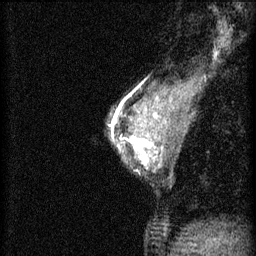
Breast MRI (dynamic contrast-enhanced), one sagittal slice; position 36 of 46 along the scan axis; 3 images stored at this slice position (order not interpretable as contrast timing); 1.5 T; TE 4.2 ms, TR 8.2 ms; 256 × 256 image matrix, field of view 180 × 180 mm. Patient: female, 44 years.
Annotated regions visible in this slice (semi-automatic segmentation, software-assisted and operator-edited):
- analysis volume of interest (the breast-tissue region the enhancement analysis was run in; not a lesion): bounding box <110,128,156,173> (left, top, right, bottom; pixels)
- tumour enhancement mask (voxels above the 70 % enhancement threshold inside the analysis volume of interest): <112,128,156,165>